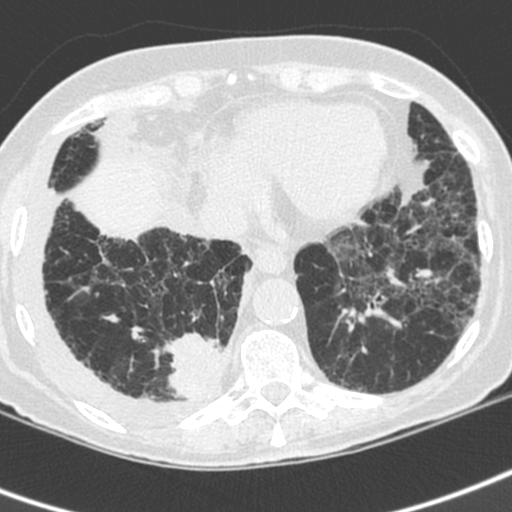
Low-dose screening chest CT, axial slice. Baseline annual screen. Lung window (W 1500 / L -600 HU). 1.3 mm slice thickness. Standard (soft-tissue) reconstruction kernel (C). Female, age 73 years at enrolment. Current smoker at enrolment.
Lesion marked by an expert reader, bounding box [x1, y1, x2, y2] px = [157, 319, 235, 406]. The exam's reader record, not a measurement of the box and not confirmed to be the same lesion: non-calcified nodule or mass ≥4 mm, right lower lobe, 35 × 30 mm, spiculated (stellate) margins, soft tissue attenuation. Official screen result: positive, change unspecified: nodule(s) >= 4 mm or enlarging nodule(s), mass(es), or other non-specific abnormalities suspicious for lung cancer. Participant outcome: lung cancer diagnosed 22 days after this screen — adenocarcinoma, NOS, right lower lobe, stage IV (AJCC 6th edition), 35 mm at pathology.